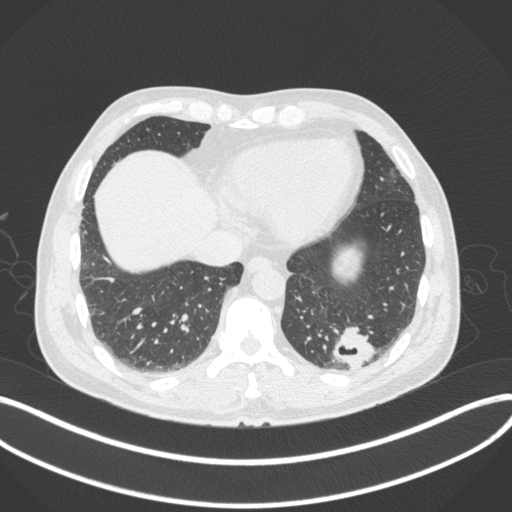
Chest CT, one axial slice. Slice 70 of 313 in the series (ordered by position). Reconstruction kernel B31f. Lung window (W 1500 / L -600 HU). 1 mm slice thickness. 512 × 512 image matrix, field of view 400 × 400 mm. Male patient, age 54 years. From the clinical record (not read from this slice): clinical TNM (as recorded): T1c N0 M1; histopathological grade: G3.
Annotated regions visible in this slice (rectangle marked by the reading radiologist):
- lung tumour (recorded histology: adenocarcinoma): bounding box (x1, y1, x2, y2) in pixels: (330, 326, 377, 371)